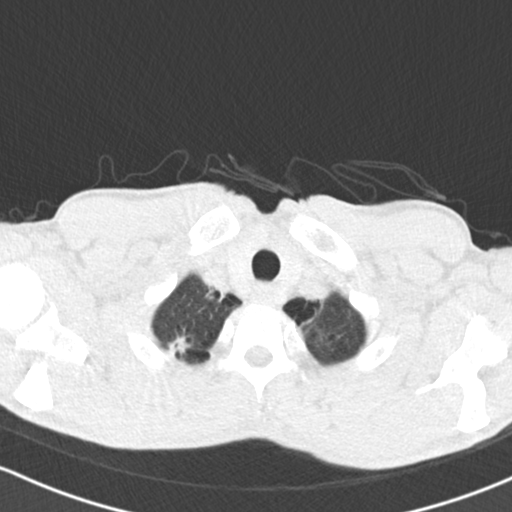
Low-dose screening chest CT, axial slice; baseline annual screen; lung window (W 1500 / L -600 HU); 2 mm slice thickness; standard (soft-tissue) reconstruction kernel (B30f). Male participant, aged 64 years at enrolment. Current smoker at enrolment.
Expert reader's lesion annotation, bounding box <150,321,203,369> (left, top, right, bottom; pixels). Screening reader's record for this exam (one nodule recorded; not confirmed to be the boxed lesion): non-calcified nodule or mass ≥4 mm, right upper lobe, 13 × 11 mm, spiculated (stellate) margins, soft tissue attenuation. Official screen result: positive, change unspecified: nodule(s) >= 4 mm or enlarging nodule(s), mass(es), or other non-specific abnormalities suspicious for lung cancer. Participant outcome: lung cancer diagnosed 161 days after this screen — adenocarcinoma, NOS, right upper lobe, poorly differentiated (G3), stage IA (AJCC 6th edition), 13 mm at pathology.